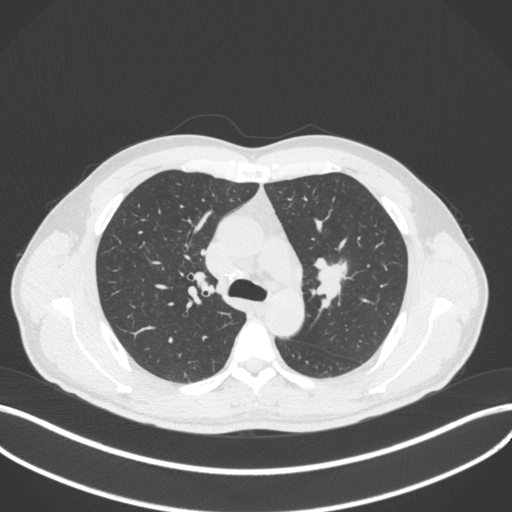
Chest CT, one axial slice. Slice 284 of 383 in the series (ordered by position). Reconstruction kernel B31f. 120 kVp. Lung window (W 1500 / L -600 HU). 512 × 512 image matrix. Patient: male, 50 years. Case-level facts recorded for this patient, not image findings: clinical TNM (as recorded): T1c N1 M1b.
Outlined on this slice (rectangle marked by the reading radiologist):
- lung tumour (recorded histology: squamous cell carcinoma): bounding box [x1, y1, x2, y2] px = [310, 257, 347, 302]